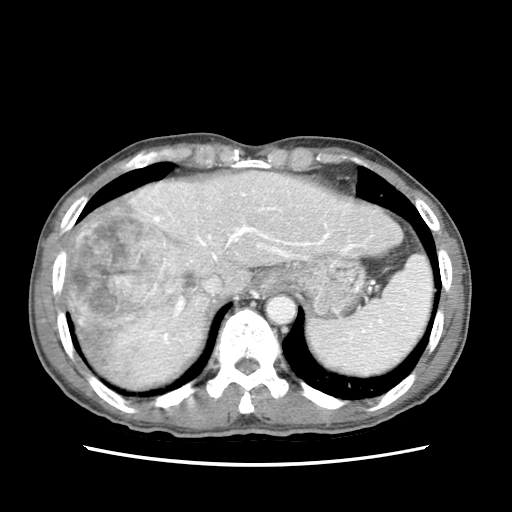
Contrast-enhanced abdominal CT (liver protocol), one axial slice. Position 59 of 79 along the scan axis. Reconstruction kernel STANDARD. 120 kVp. Soft-tissue window (W 400 / L 40 HU). 2.5 mm slice thickness. 512 × 512 image matrix. Case-level facts recorded for this patient, not image findings: diagnosis: hepatocellular carcinoma (patient treated with transarterial chemoembolisation; whether this scan precedes or follows treatment is not stated here); TNM stage (as recorded): Stage-IIIB; Child-Pugh class: A.
Outlined on this slice (semi-automatically segmented with operator editing):
- abdominal aorta: box from (x=267, y=295) to (x=295, y=323) px
- liver parenchyma outside the tumour (the mass and vessels are separate outlines, so this box may not span the whole liver): (x=60, y=172)–(x=402, y=388)
- mass: (x=63, y=183)–(x=197, y=386)
- liver vessels: (x=151, y=188)–(x=377, y=347)